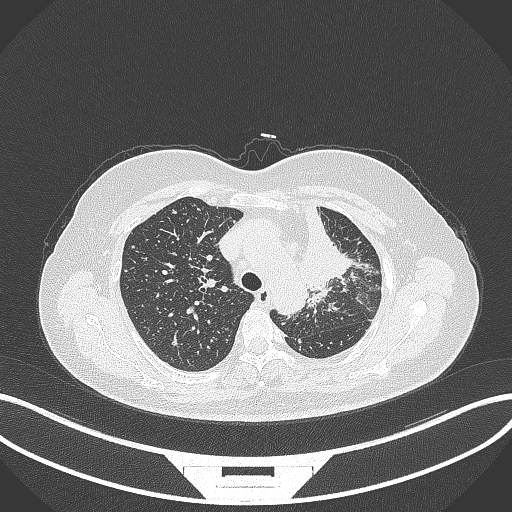
Chest CT, one axial slice; slice 247 of 348 in the series (ordered by position); 120 kVp; lung window (W 1500 / L -600 HU); 1 mm slice thickness; 512 × 512 image matrix, field of view 400 × 400 mm. Patient: female, 49 years. Case-level facts recorded for this patient, not image findings: clinical TNM (as recorded): T1c N0 M1.
Outlined on this slice (rectangle marked by the reading radiologist):
- lung tumour (recorded histology: adenocarcinoma): bounding box (x1, y1, x2, y2) in pixels: (289, 192, 356, 293)